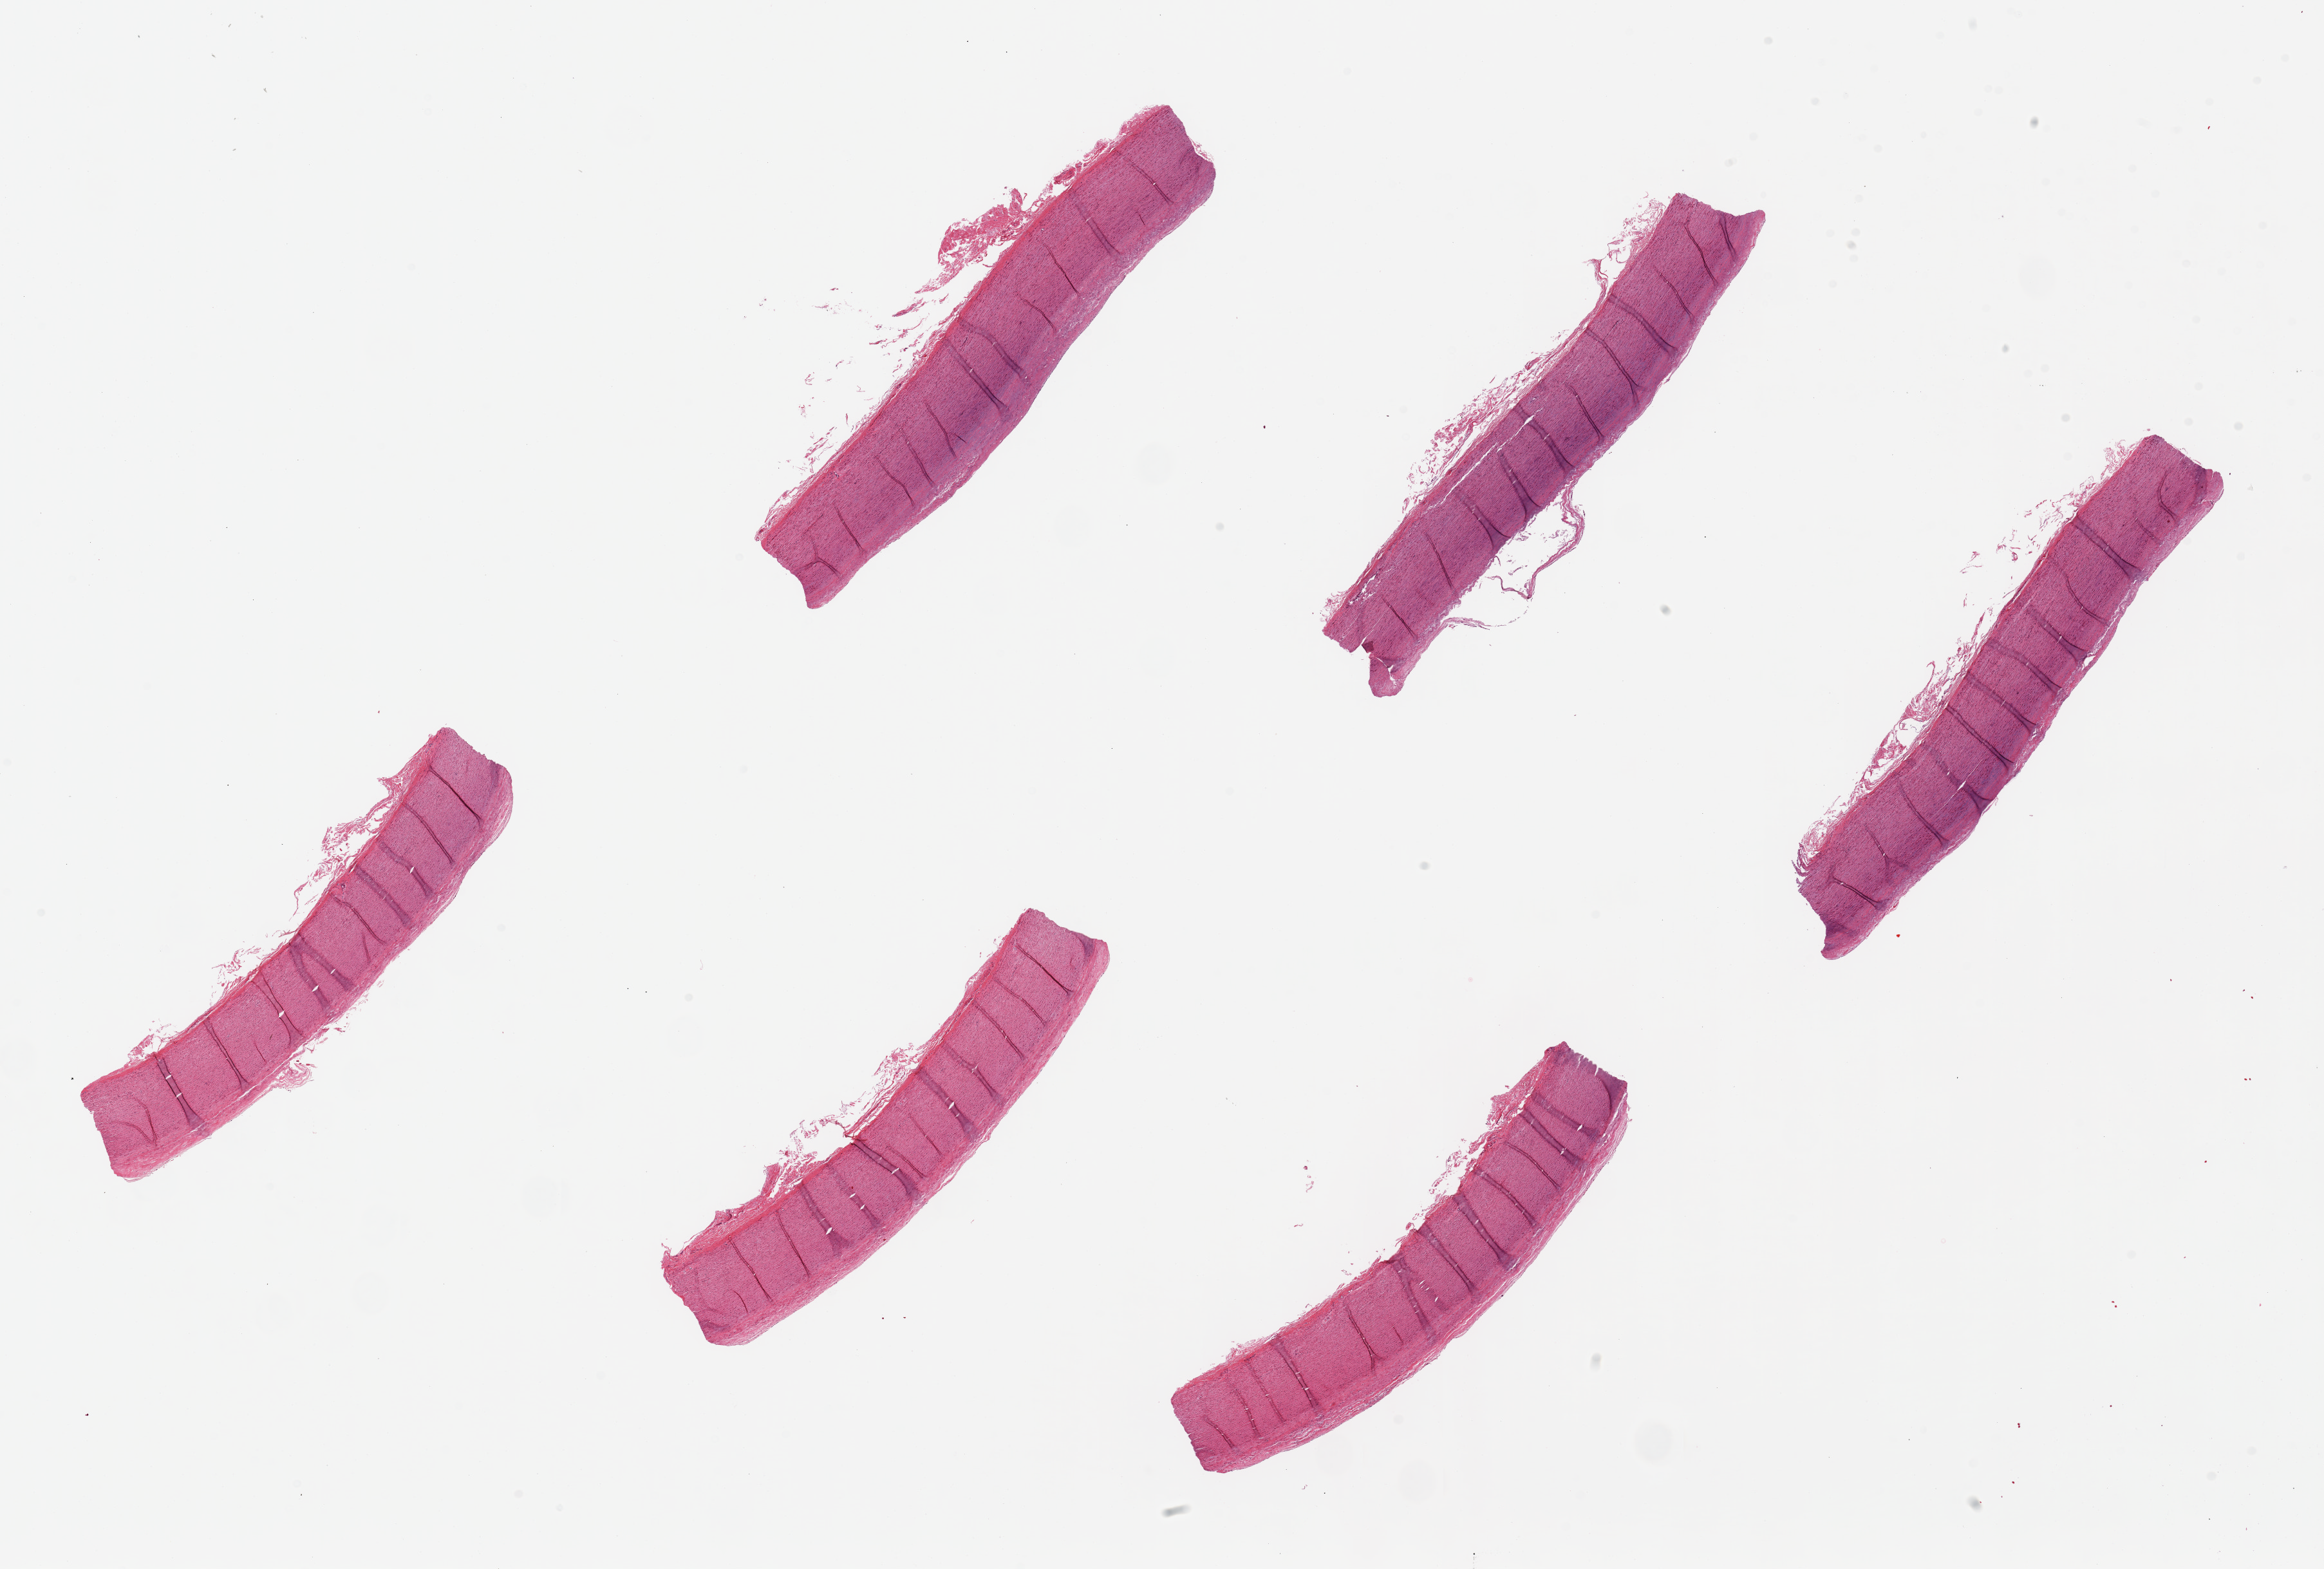
H&E whole-slide image, brightfield — a low-resolution overview of the entire scanned area, about 28.5 x 19.3 mm. PAXgene-fixed paraffin-embedded (PFPE) section. Target tissue: aorta. Donor tissue sample. Donor: male.
* reviewer comment on this tissue sample: 6 pieces, up to 8x2mm; Mild plaque formation